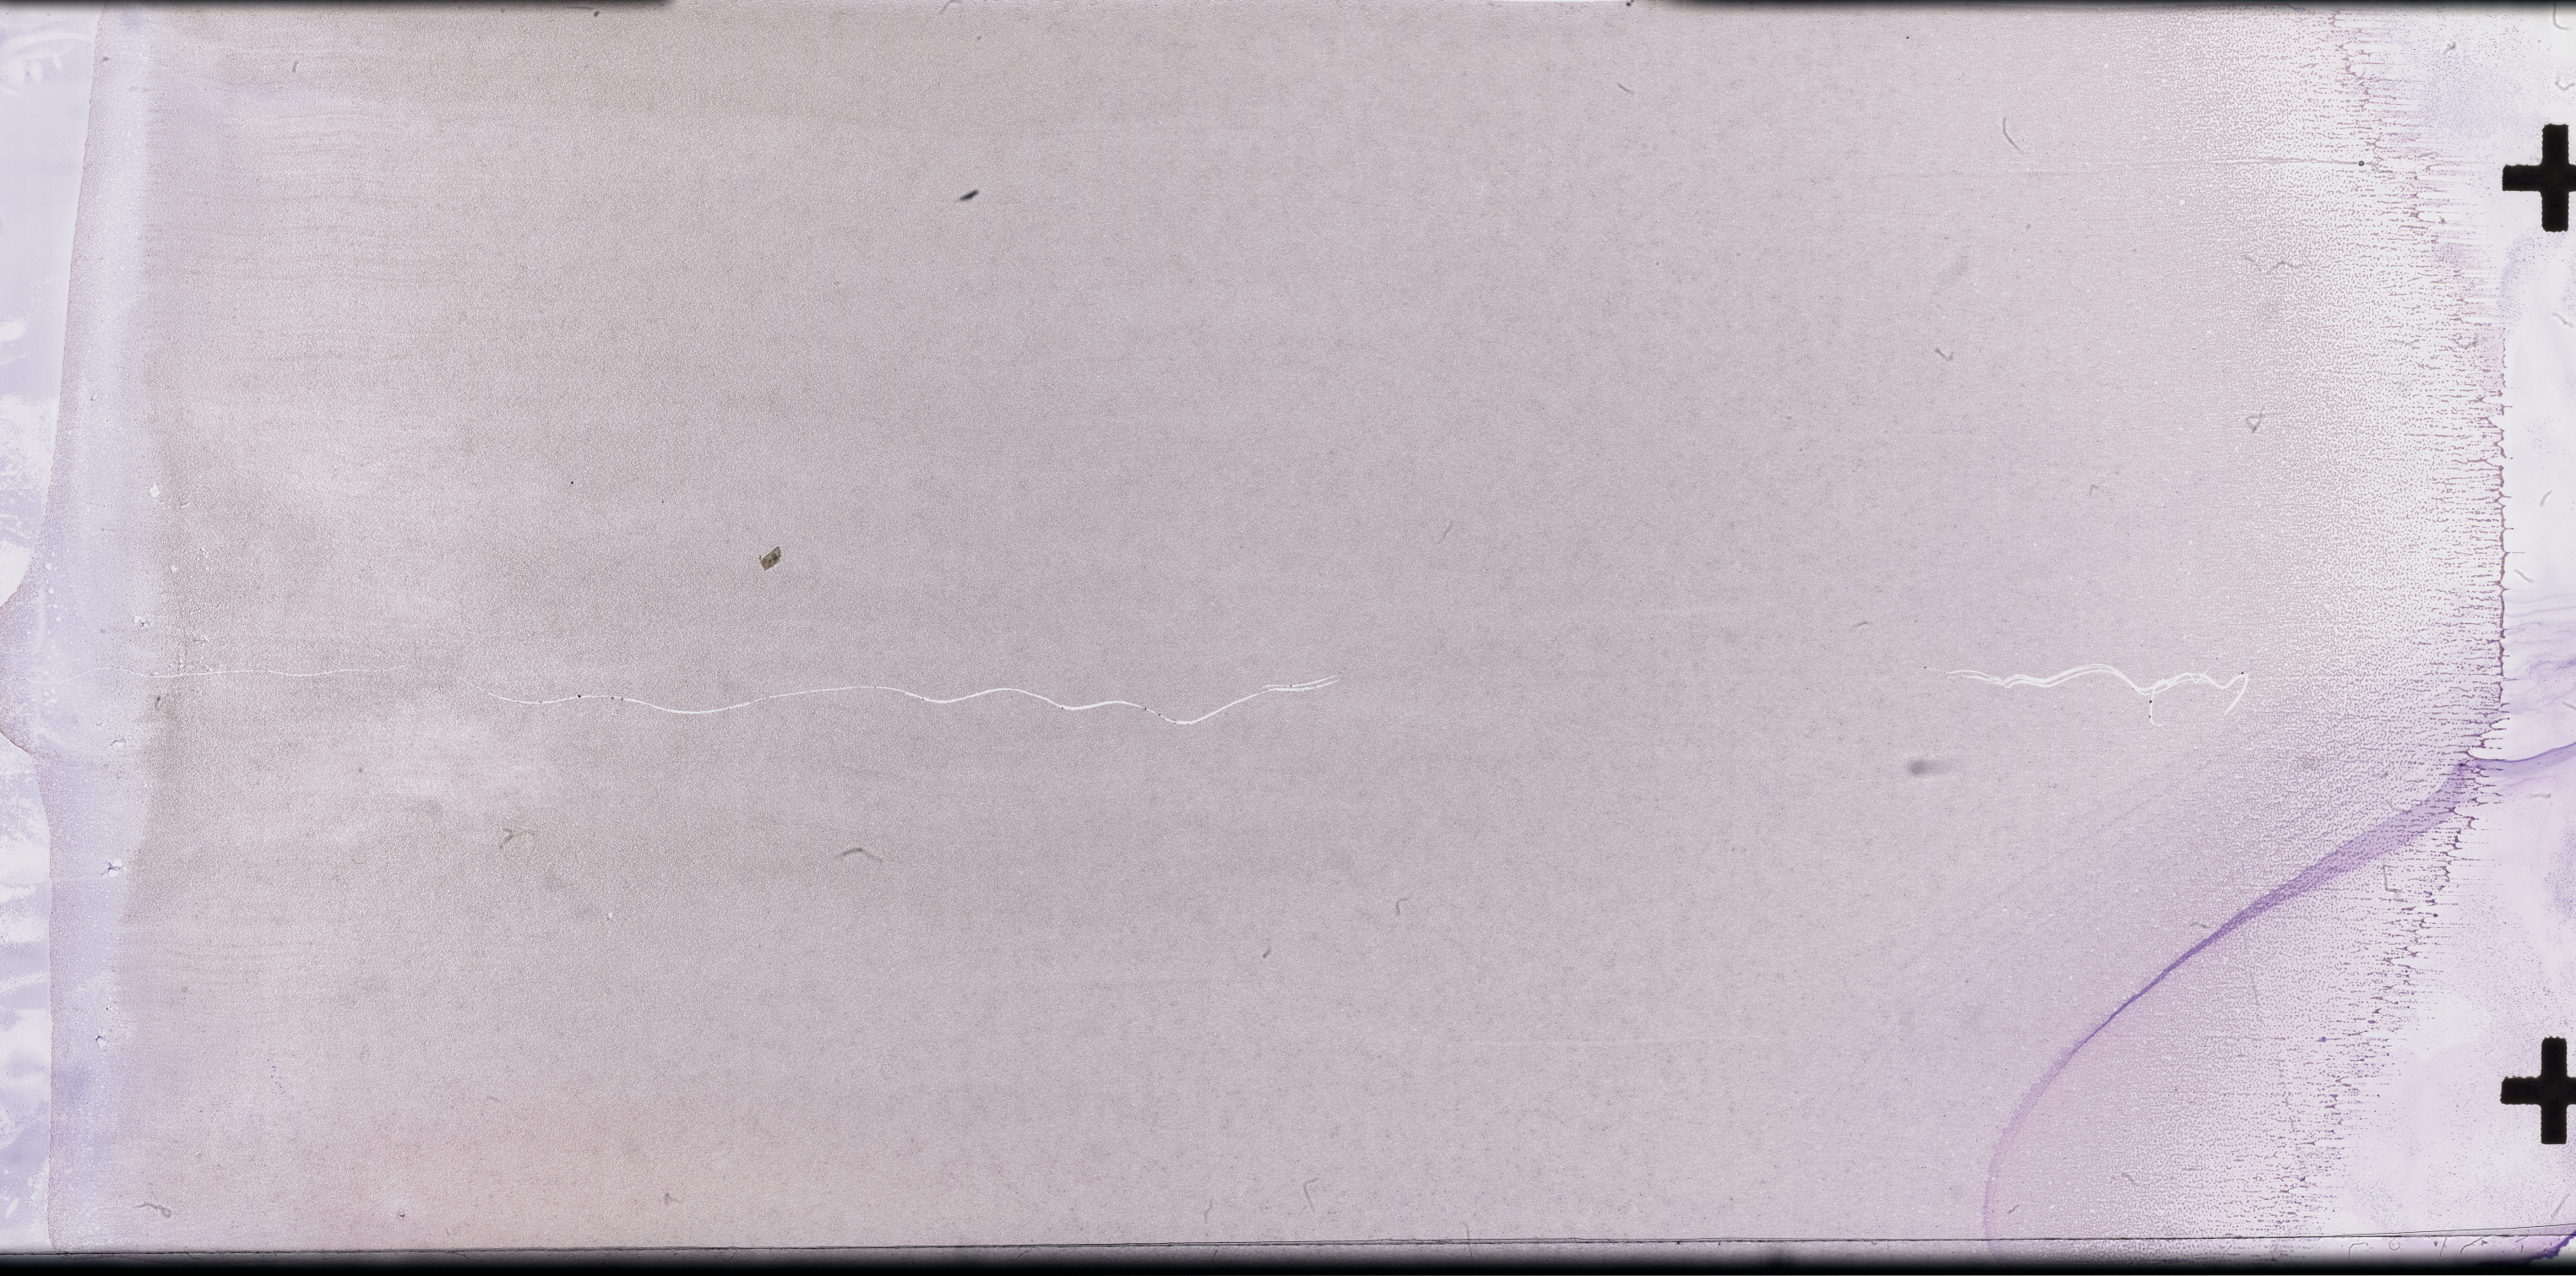
Wright–Giemsa-stained whole blood smear, whole-slide image — shown as a low-resolution overview of the whole scanned area (about 49.3 x 24.4 mm), smear from an EDTA sample. Female patient.
From a patient with: Plasma Cell Myeloma.